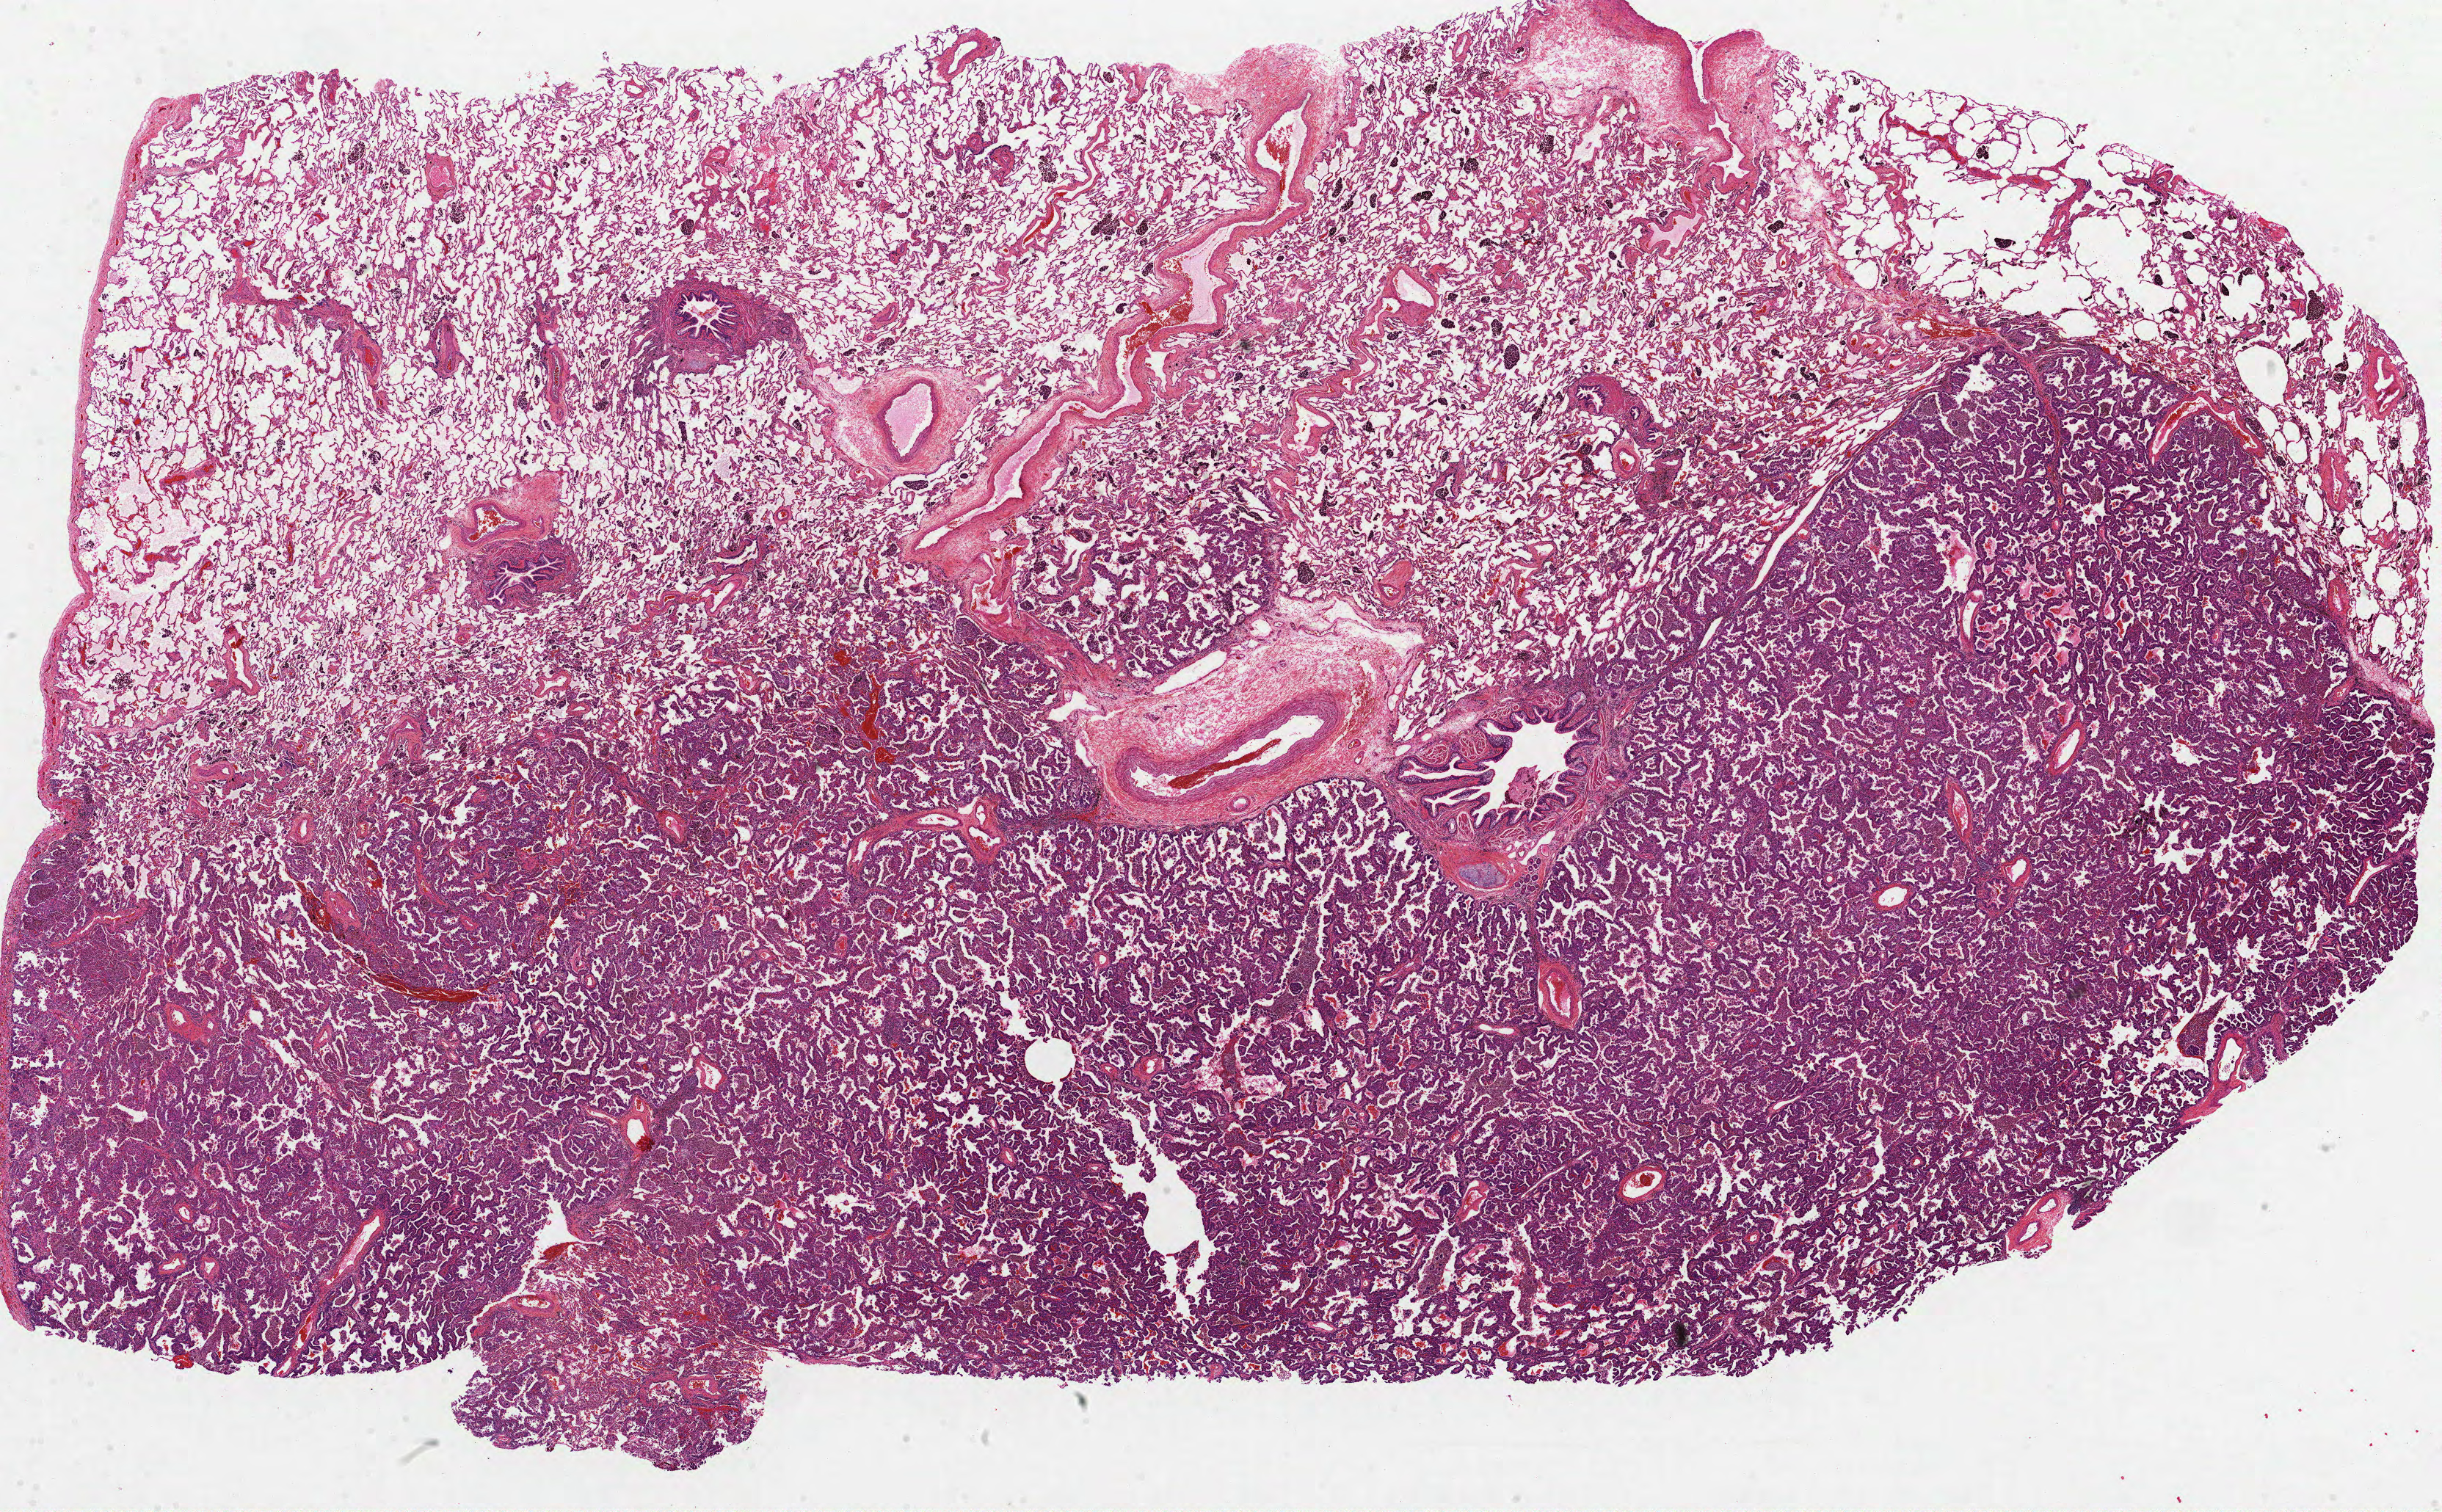
Whole-slide histology image, H&E-stained, low-resolution overview of the scanned area, about 26.8 x 16.6 mm (from a 40x scan). FFPE section. Primary tumour sample from the lung. Female patient; age at initial diagnosis 51 years.
- pathologic diagnosis: Adenocarcinoma, NOS (upper lobe, lung)
- AJCC pathologic stage: IIB (5th edition)
- laterality: left